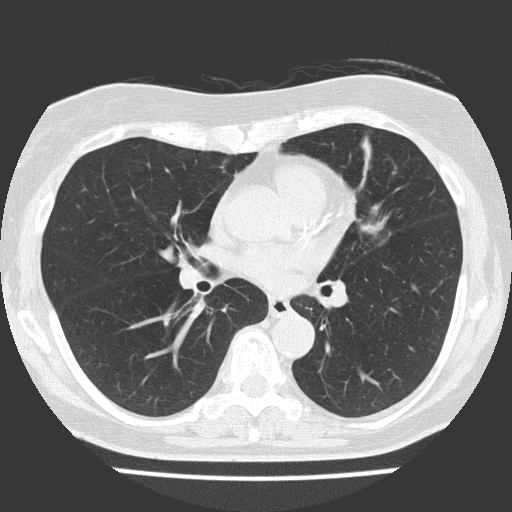
Low-dose screening chest CT, one axial slice; 120 kVp; lung window (W 1500 / L -600 HU); 2 mm slice thickness; 512 × 512 image matrix.
Annotated regions visible in this slice (outlined manually by an expert reader):
- lesion 1 (tumor, upper lobe of left lung): bounding box (x1, y1, x2, y2) in pixels: (360, 217, 387, 234)